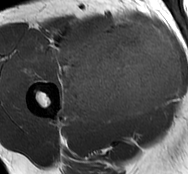
MRI of an extremity soft-tissue mass, one axial slice; slice 42 of 93 in the series (ordered by position); MR volume resampled by the dataset authors to the PET/CT grid (not the native acquisition matrix); 3.27 mm slice thickness; 188 × 174 image matrix. Male patient. From the clinical record (not read from this slice): histological type: undifferentiated - pleiomorphic; grade: high; site of the primary tumour: right thigh.
Structures marked on this image (expert contour drawn on MRI and transferred to this co-registered scan by the dataset authors):
- gross tumour volume including surrounding oedema: box from (x=56, y=19) to (x=183, y=127) px
- gross tumour volume (mass): (x=70, y=19)–(x=183, y=121)